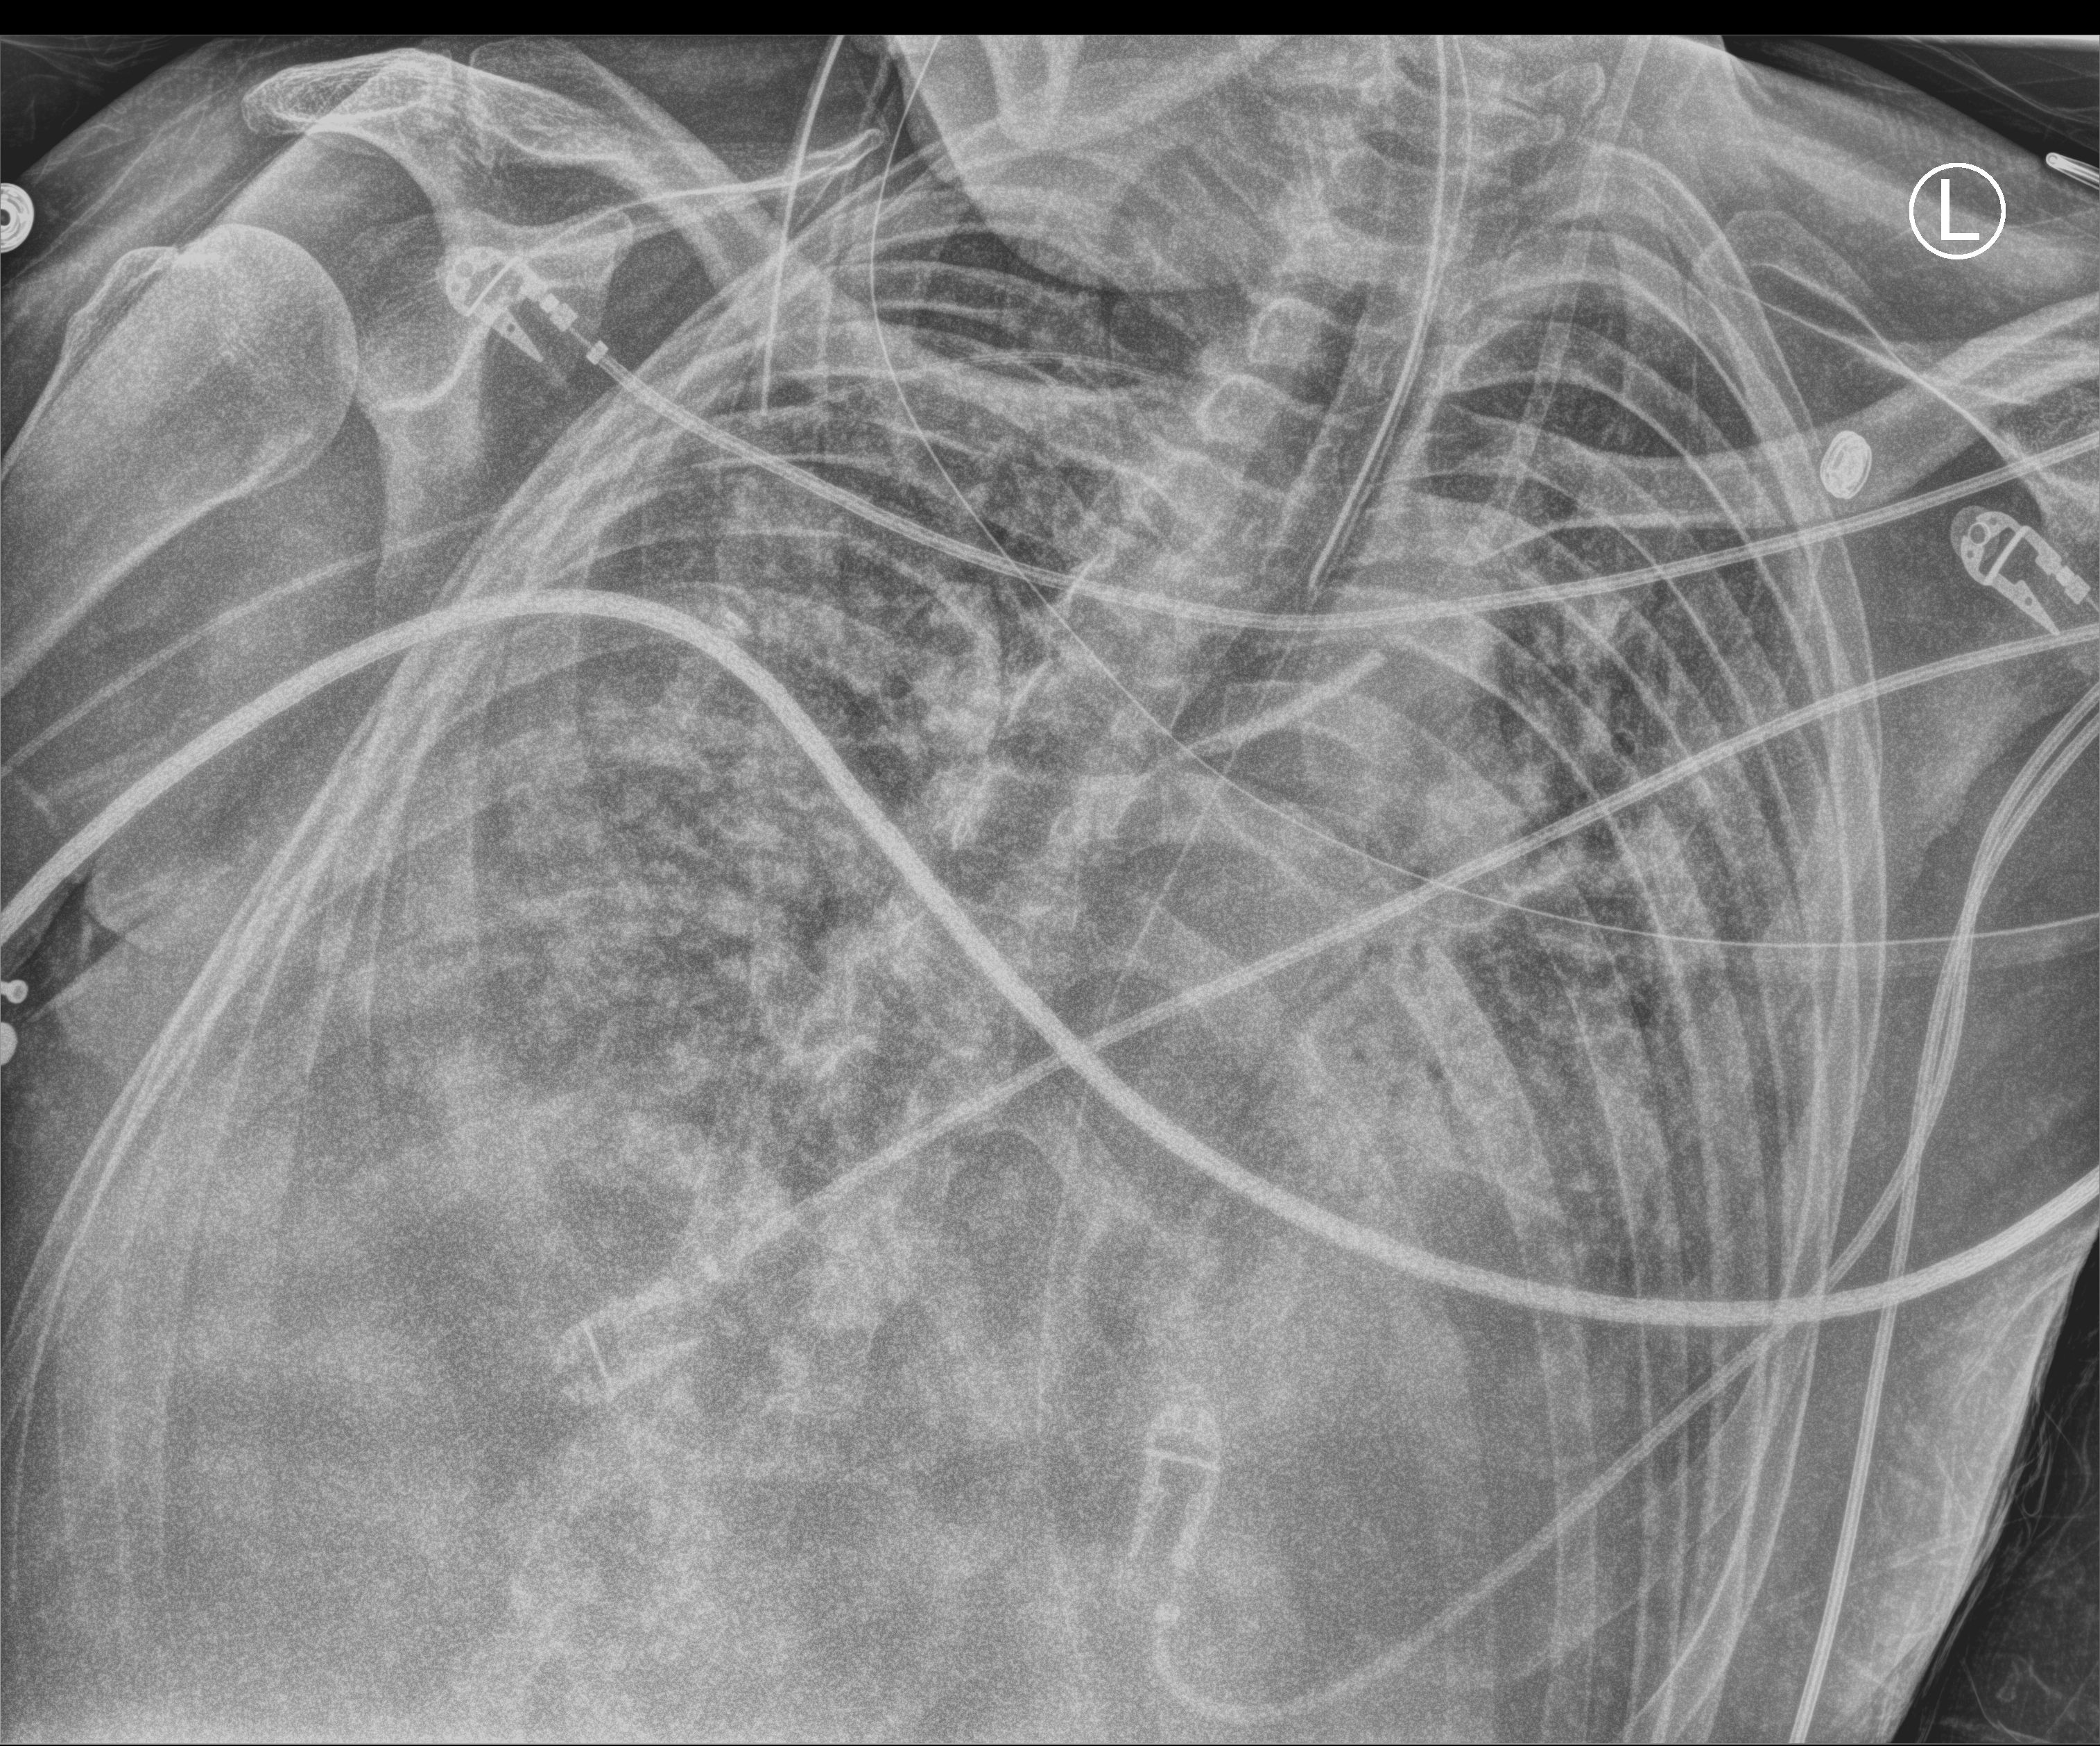
Bedside chest radiograph (computed radiography), anteroposterior (AP) projection. Male patient hospitalised with COVID-19, age 18–59 years.
From the hospital-stay record, not from the radiograph (when in the stay this image was taken is not recorded):
- other chronic lung disease (admission record): no